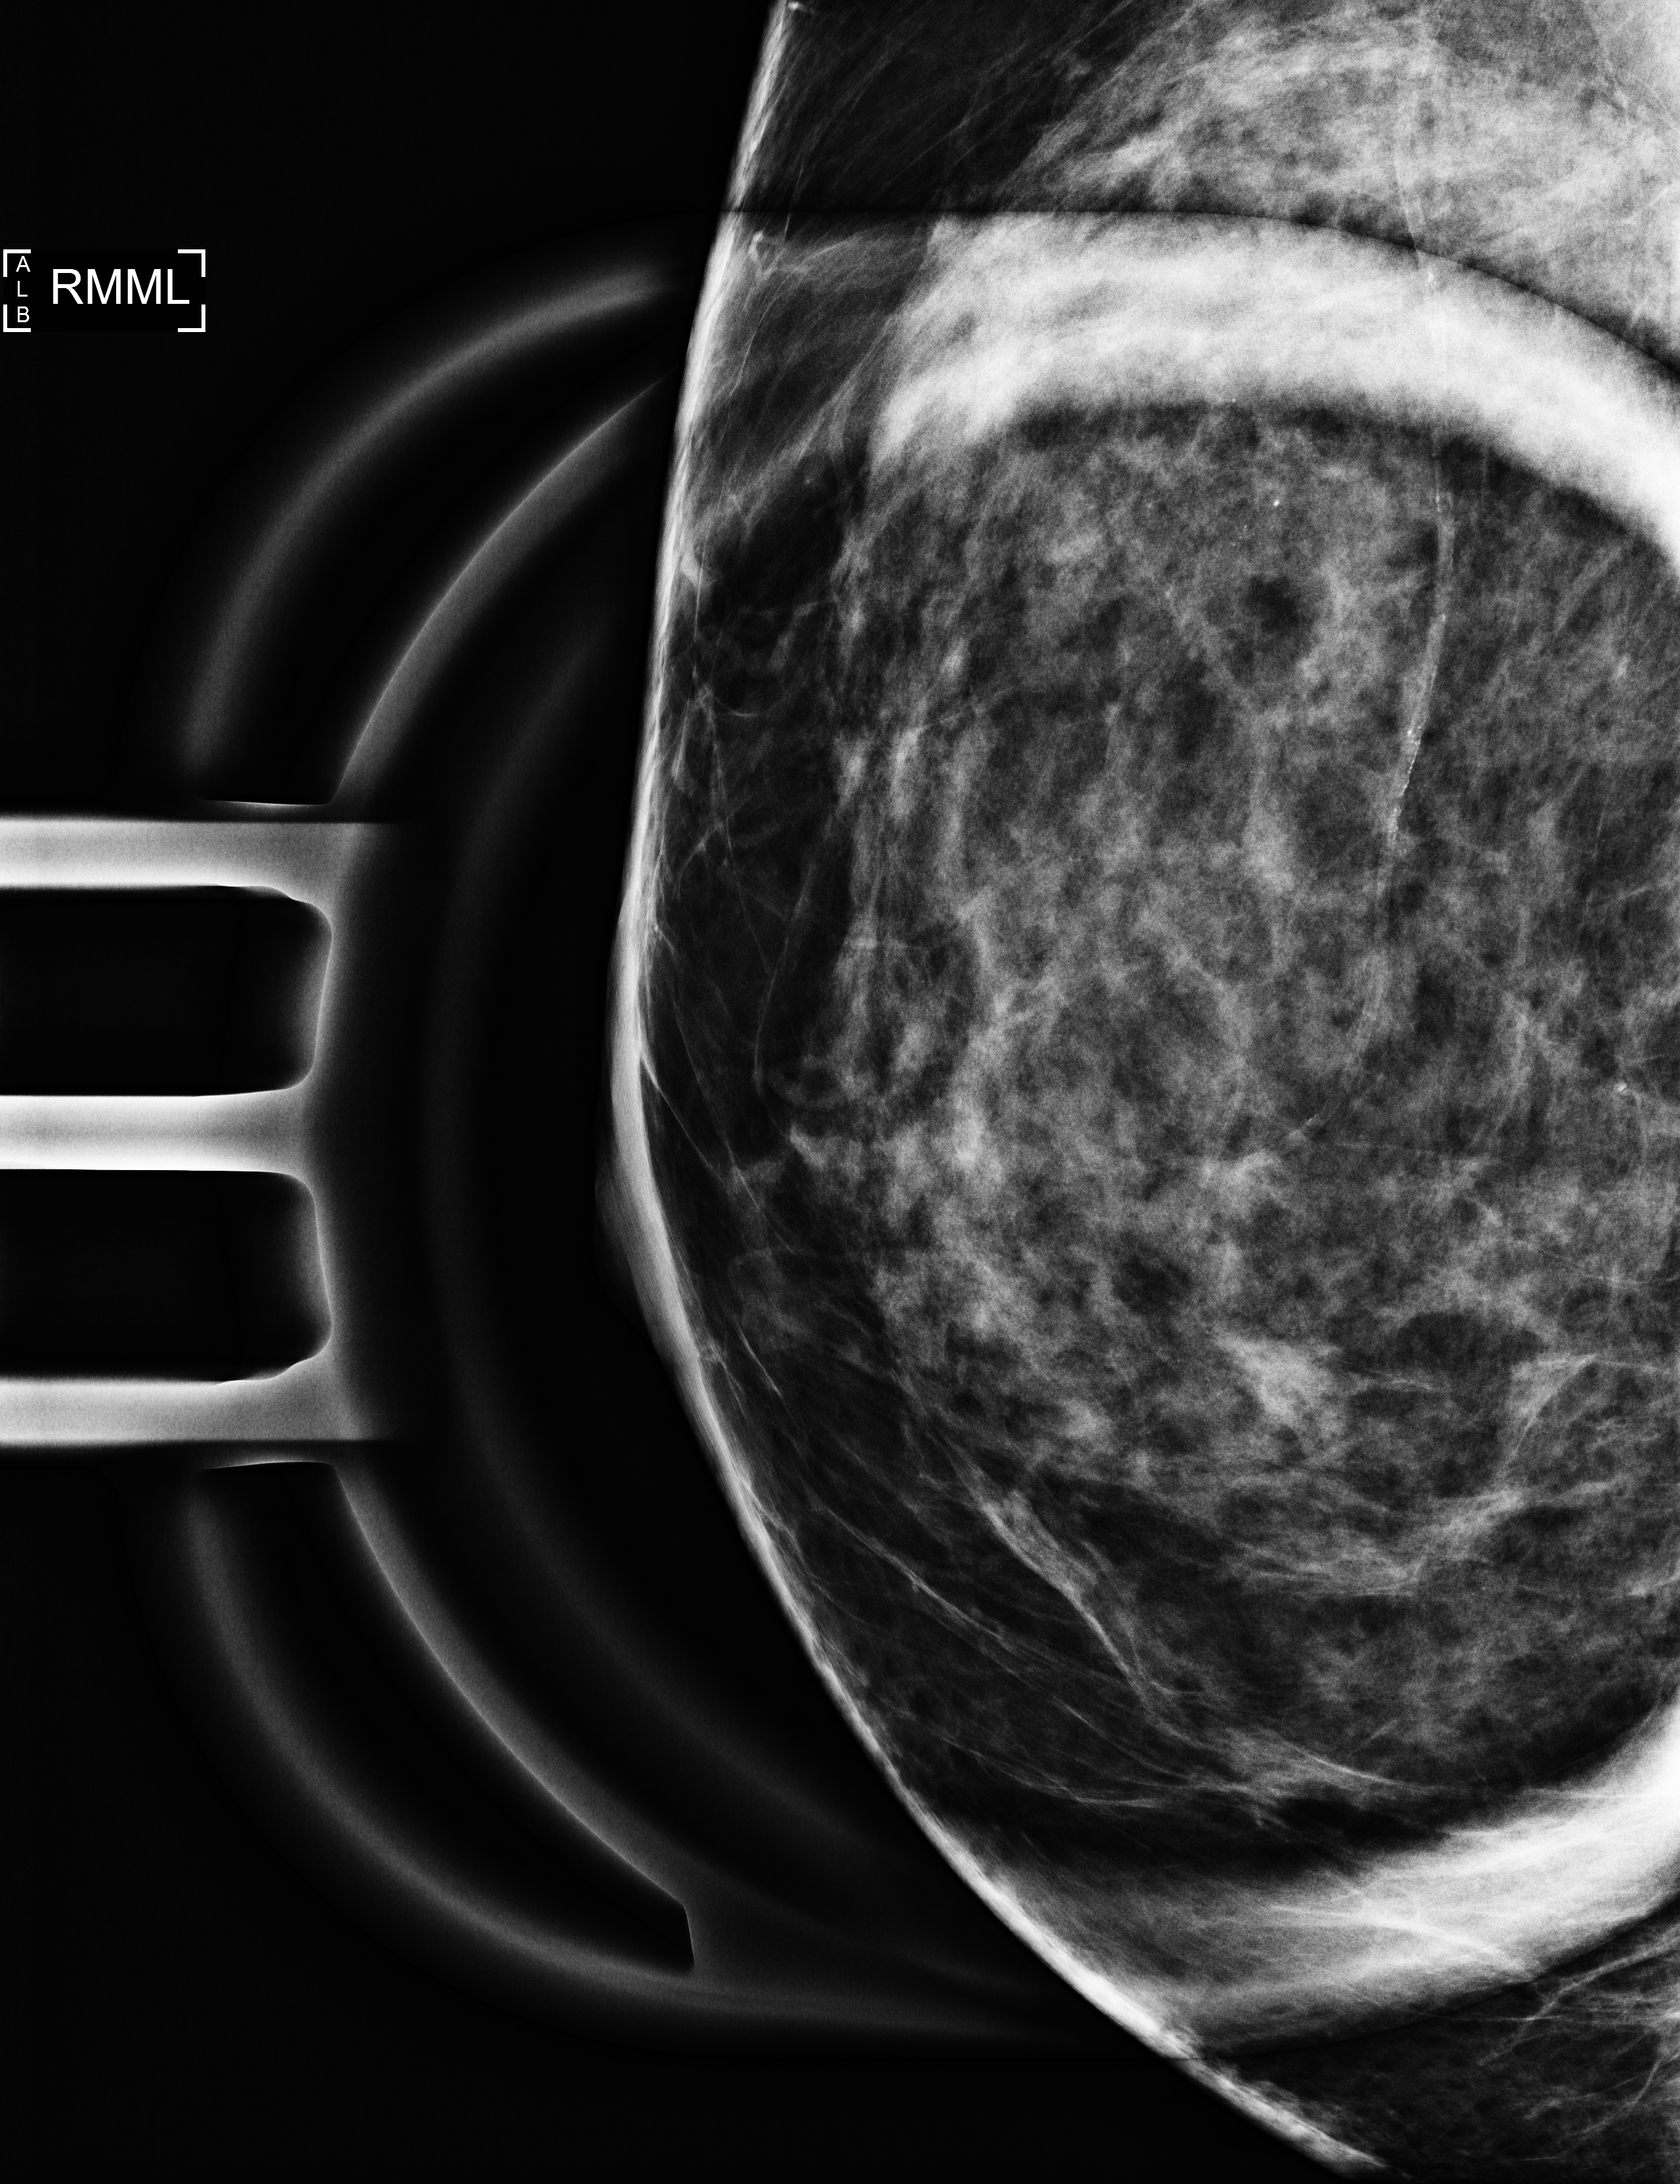
Additional work-up view; compressed breast thickness 48 mm. Patient: female, 55 years.
Image type: full-field digital mammogram. Breast: right. Projection: ML view, magnification.